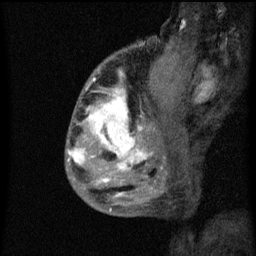
Breast MRI (dynamic contrast-enhanced), one sagittal slice. Position 19 of 60 along the scan axis. Dynamic contrast-enhanced series, image 2 of 3 at this slice position (ordered by acquisition). 1.5 T. TE 4.2 ms, TR 8 ms. 2 mm slice thickness. 256 × 256 image matrix, field of view 180 × 180 mm. Patient: female, 50 years.
Outlined on this slice (semi-automatically segmented with operator editing):
- analysis volume of interest (the breast-tissue region the enhancement analysis was run in; not a lesion): box from (x=66, y=64) to (x=141, y=187) px
- tumour enhancement mask (voxels above the 70 % enhancement threshold inside the analysis volume of interest): (x=67, y=72)–(x=141, y=183)